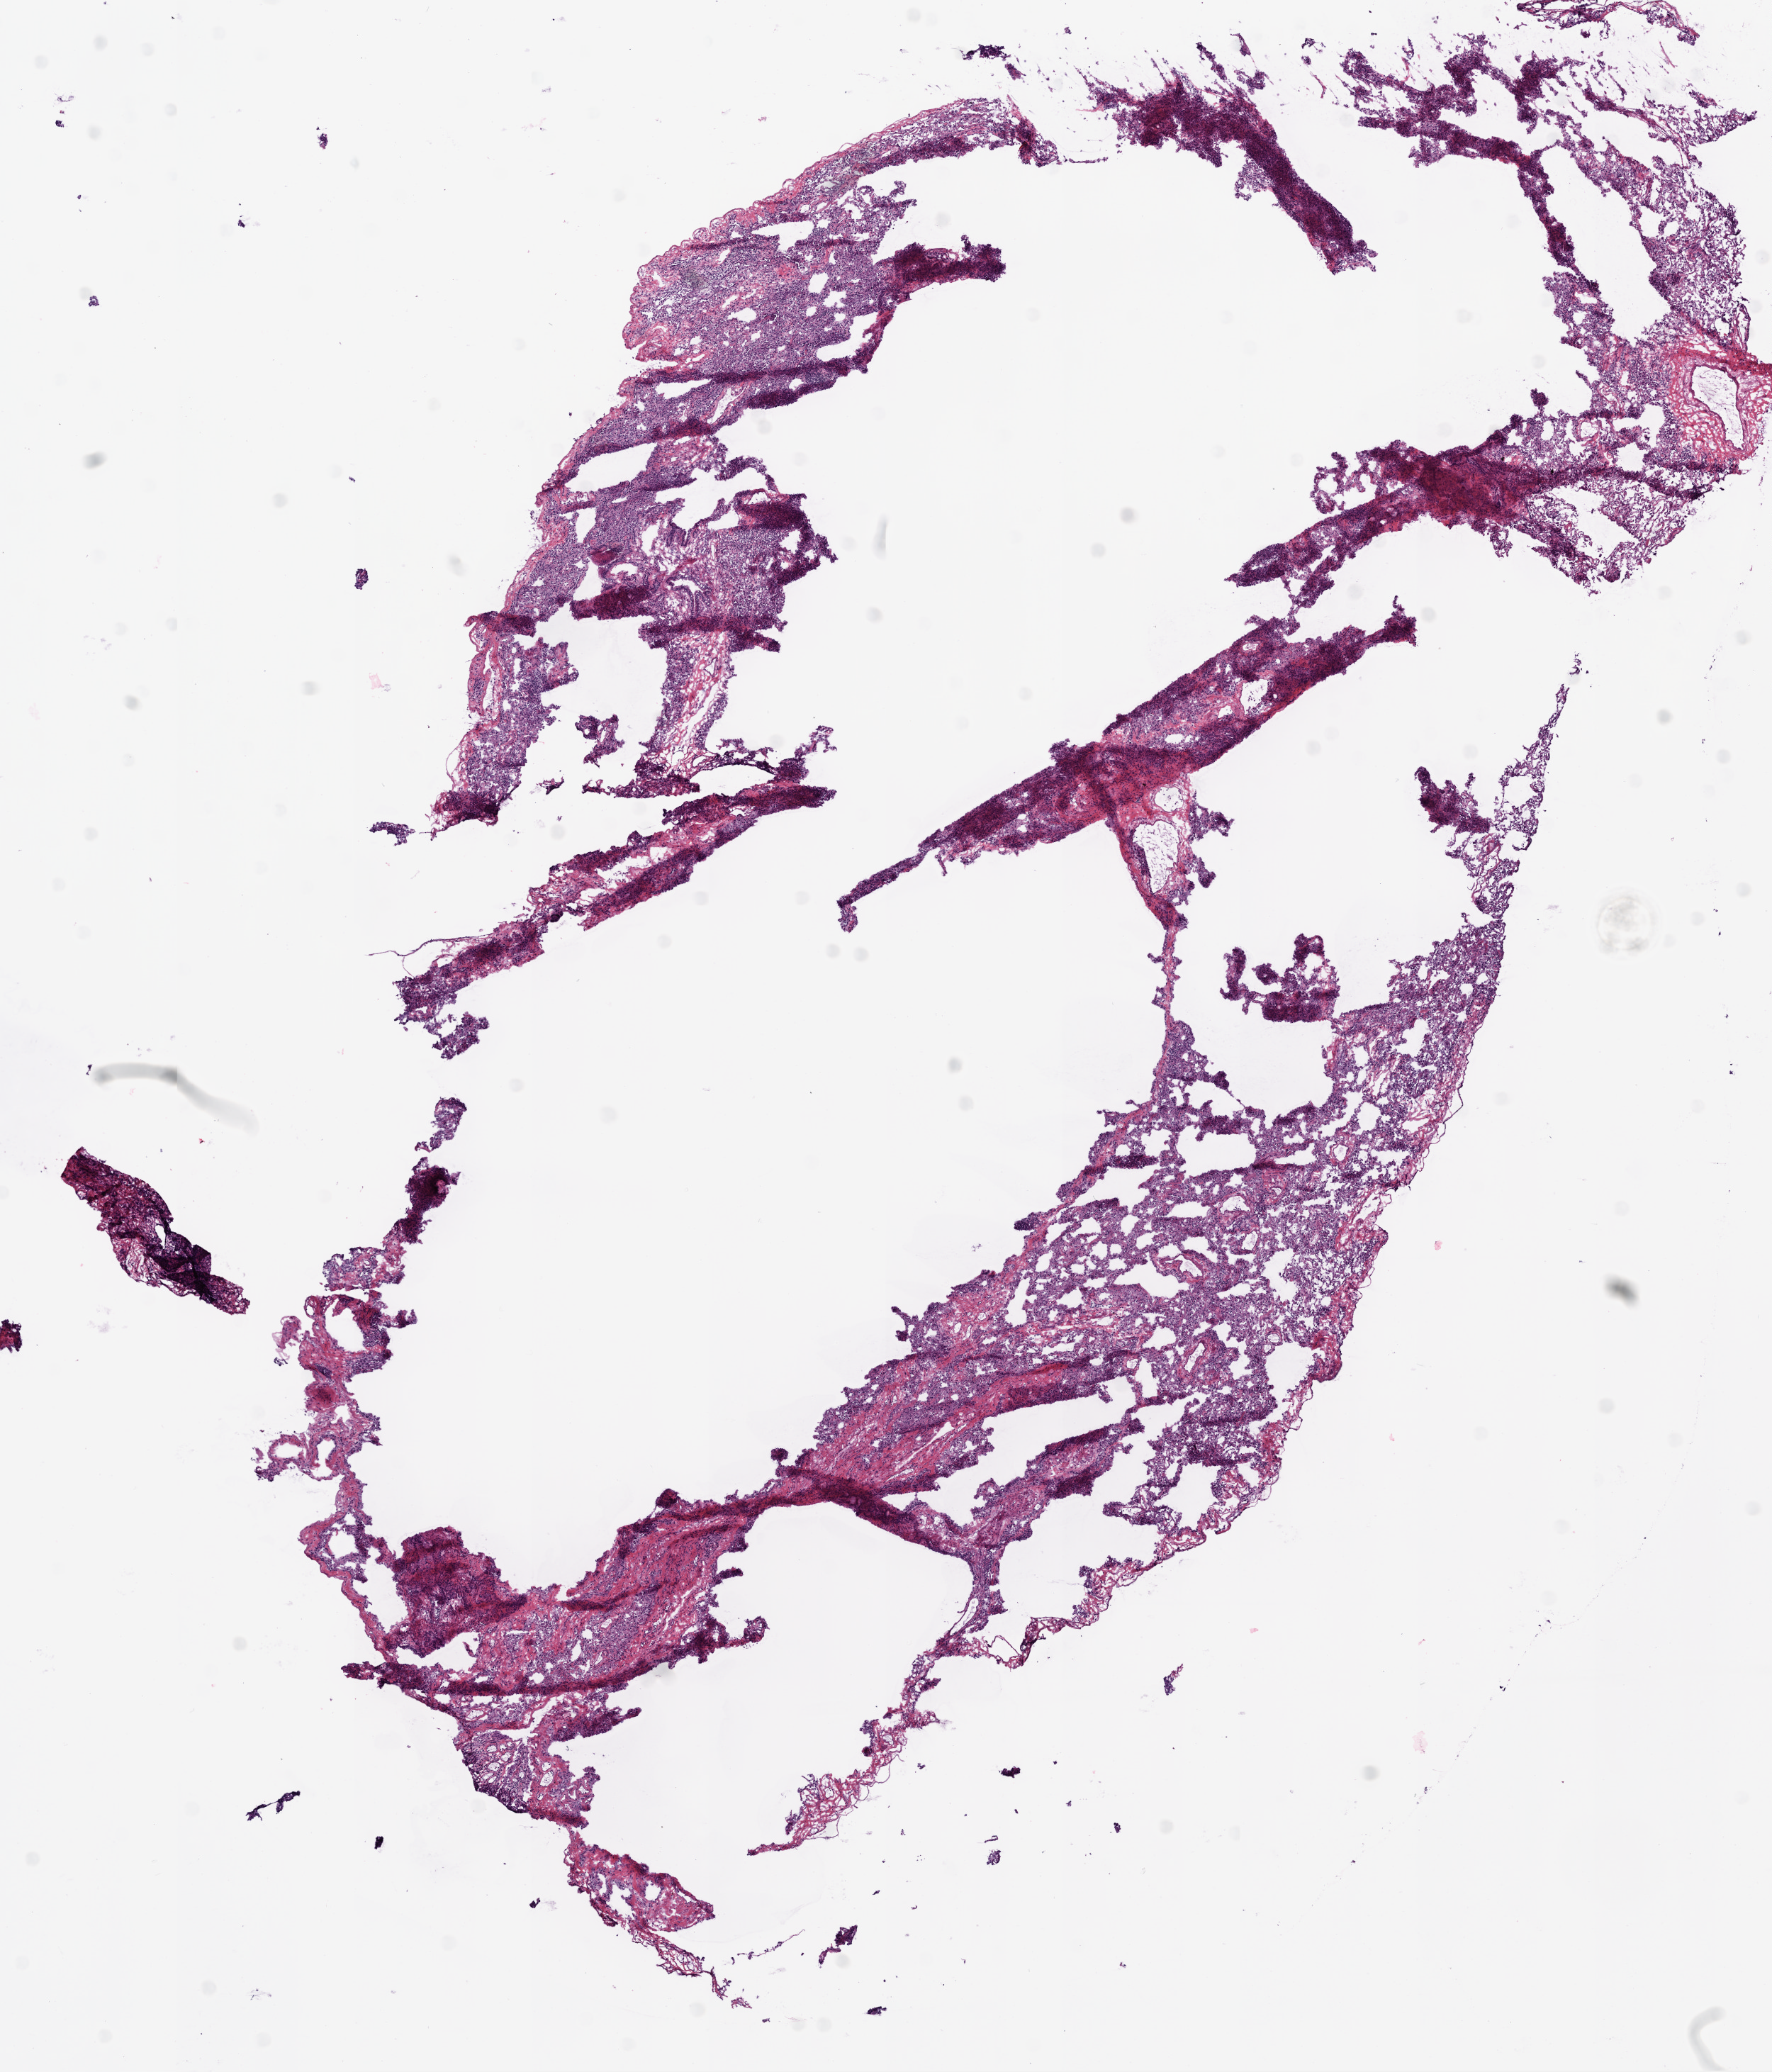
H&E whole-slide image — shown as a low-resolution overview of the whole scanned area (about 10.0 x 11.7 mm, slide scanned at 20x). Frozen section from the bottom of the tissue portion. Sample: solid tissue normal (non-tumour tissue), lung. Male patient; age at initial diagnosis 64 years.
This section: solid tissue normal sample (biorepository sample class). Patient diagnosis: Squamous cell carcinoma, NOS (upper lobe, lung).